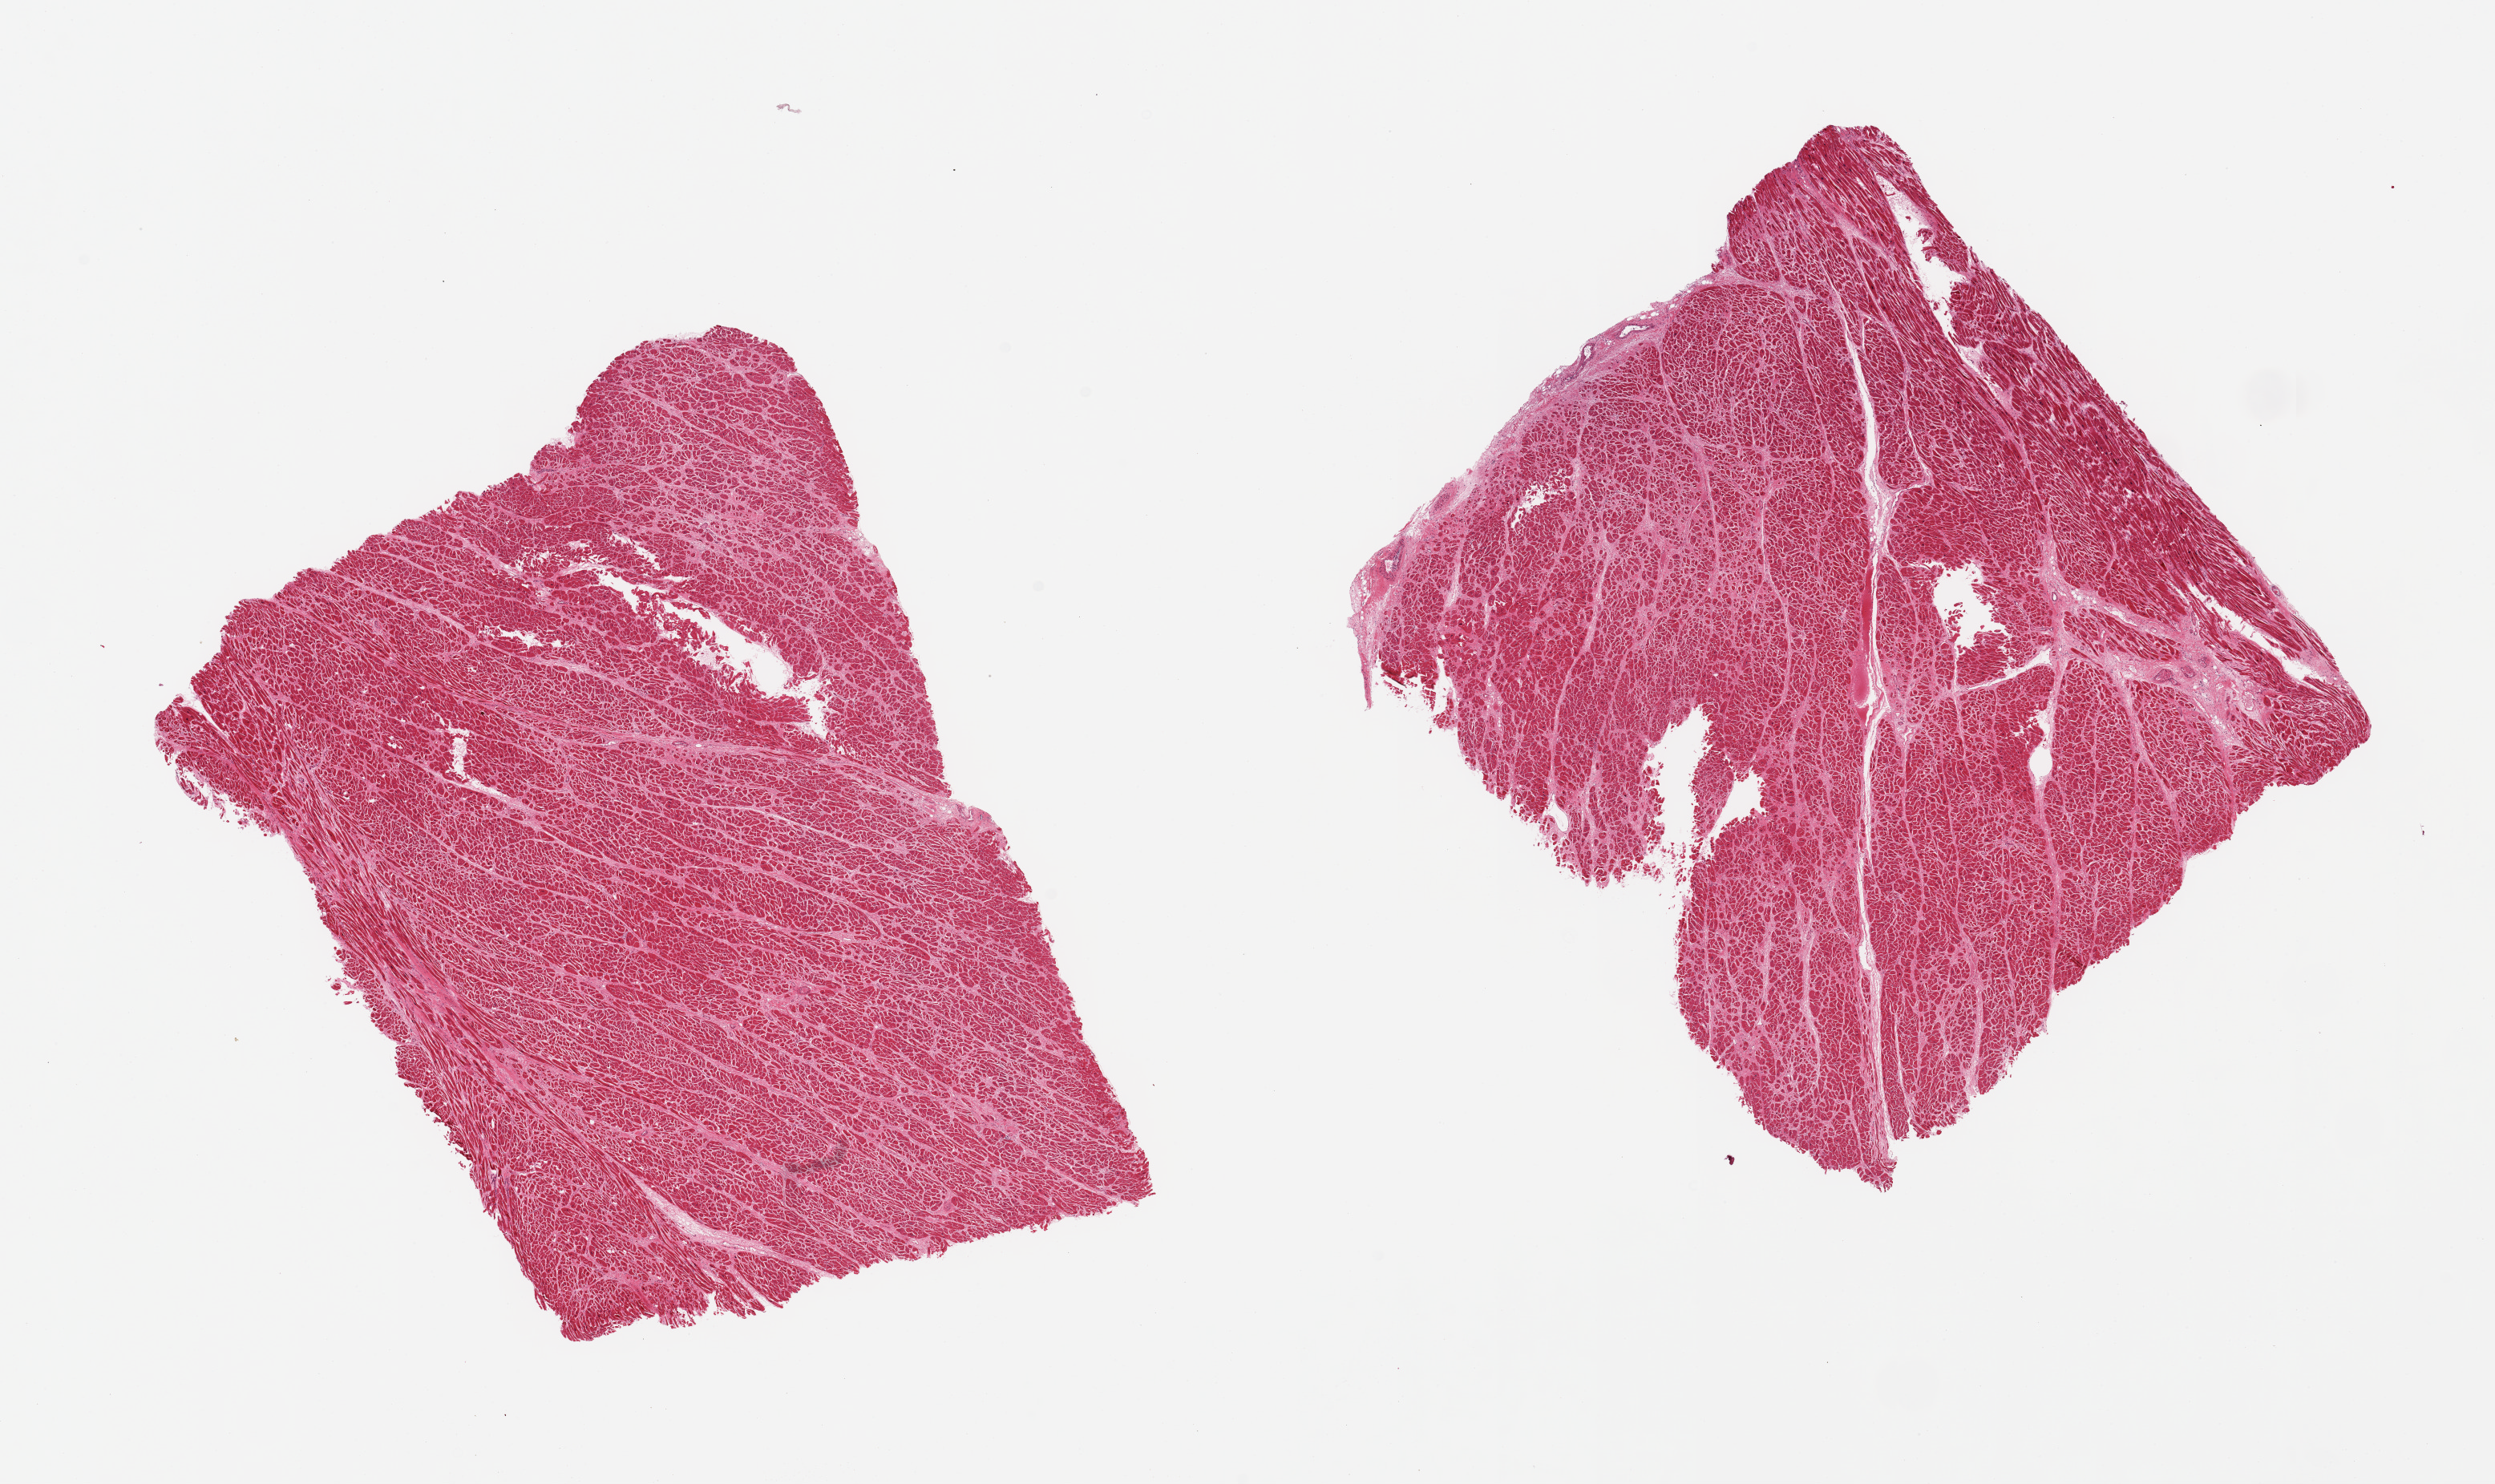
Whole-slide image, hematoxylin and eosin (H&E) stain, shown as a low-resolution overview of the whole scanned area (about 24.6 x 14.6 mm). PAXgene-fixed paraffin-embedded (PFPE) section. Section of heart (target tissue). Tissue donor sample. Male donor.
• review note (as recorded): 2 pieces; interstitial/patchy fibrosis, myocyte hypertrophy